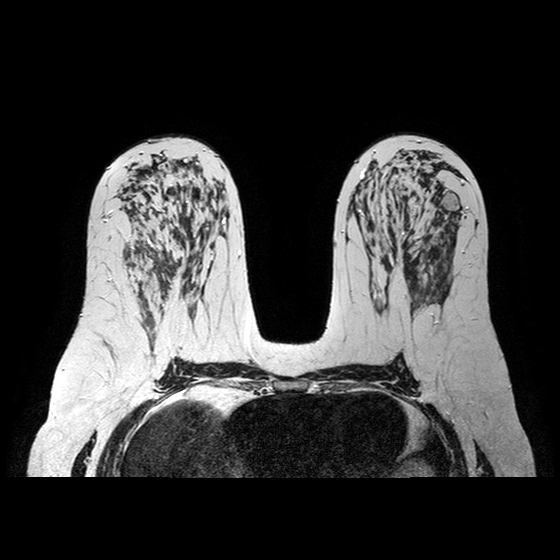
Breast MRI examination; 2 images, each one mid-volume slice chosen by position.
Image 1: fluid-sensitive (T2/STIR) axial slice, series "T2W_TSE SENSE", slice 43 of 84.
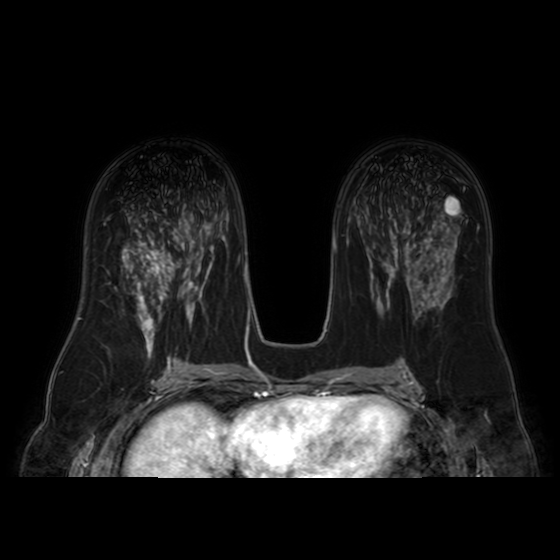
Image 2: post-contrast dynamic axial slice, series "AX BLISS_AUTO SENSE", slice 43 of 84, dynamic phase 5 of 8, 4 mm slice thickness.
Pathology recorded for this patient (not read from these images): pathology diagnosis: benign (right breast).